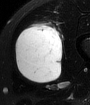
MRI of an extremity soft-tissue mass, one axial slice. Position 28 of 65 along the scan axis. T2-weighted fat-saturated. MR volume resampled by the dataset authors to the PET/CT grid (not the native acquisition matrix). 3.27 mm slice thickness. 90 × 105 image matrix. Male patient. From the clinical record (not read from this slice): histological type: mixoid liposarcoma; grade: low; site of the primary tumour: left thigh.
Annotated regions visible in this slice (expert contour drawn on MRI and transferred to this co-registered scan by the dataset authors):
- gross tumour volume (mass): bounding box <14,23,62,83> (left, top, right, bottom; pixels)